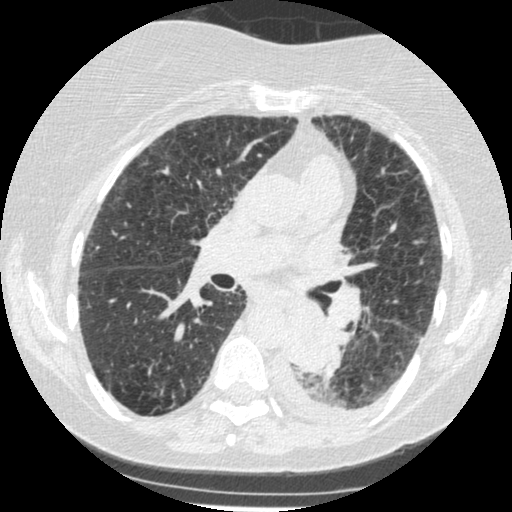
Low-dose screening chest CT, one axial slice. 120 kVp. Lung window (W 1500 / L -600 HU). 1.25 mm slice thickness. 512 × 512 image matrix, field of view 310 × 310 mm.
Annotated regions visible in this slice (manually delineated by an expert):
- lesion 1 (tumor, lower lobe of left lung): bounding box (x1, y1, x2, y2) in pixels: (285, 307, 339, 374)